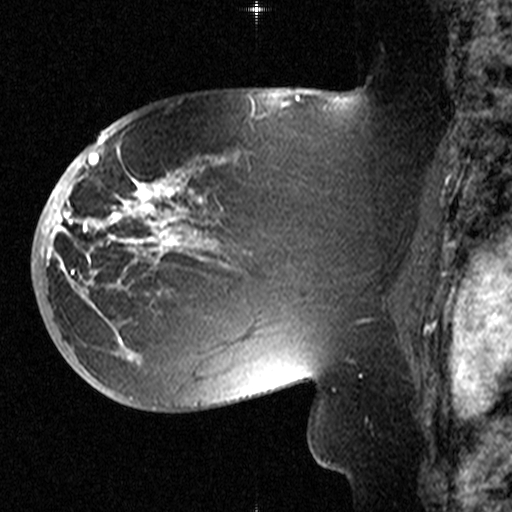
Breast MRI (dynamic contrast-enhanced), one sagittal slice; slice 27 of 44 in the series (ordered by position); dynamic contrast-enhanced study with each time point stored as its own series, time point 2 of 3 at this slice position (early post-contrast, ordered by acquisition time); 1.5 T; TE 4.5 ms, TR 11 ms; 3.27 mm slice thickness; 512 × 512 image matrix, field of view 200 × 200 mm. Female patient, age 53 years. Case-level facts recorded for this patient, not image findings: setting: breast cancer imaged before/during neoadjuvant chemotherapy; receptor status: HR-positive, HER2-negative.
Outlined on this slice (semi-automatic segmentation, software-assisted and operator-edited):
- analysis volume of interest (the breast-tissue region the enhancement analysis was run in; not a lesion): bounding box <58,154,311,367> (left, top, right, bottom; pixels)
- tumour enhancement mask (voxels above the 90 % enhancement threshold inside the analysis volume of interest): <58,176,207,342>